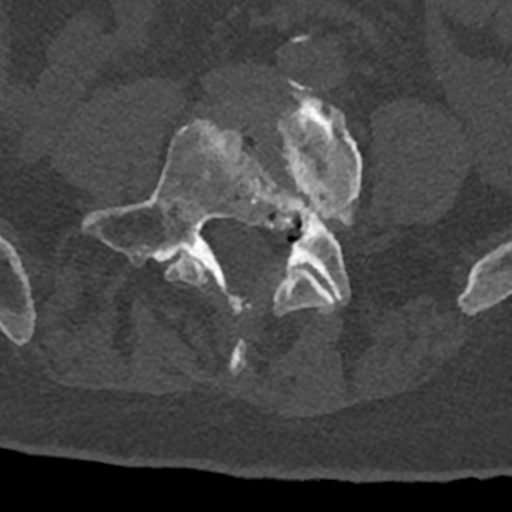
CT including the spine, one axial slice. Position 222 of 797 along the scan axis. 120 kVp. Bone window (W 1800 / L 400 HU). 0.5 mm slice thickness. 512 × 512 image matrix, field of view 160 × 160 mm. Male patient, age 74 years. From the clinical record (not read from this slice): primary cancer: renal.
Structures marked on this image (semi-automatically segmented with operator editing):
- L4 vertebra: bounding box <165,83,362,375> (left, top, right, bottom; pixels)
- L5 vertebra: <81,120,351,312>